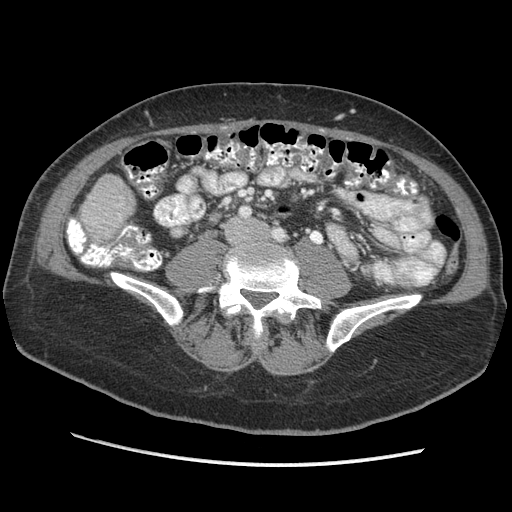
Contrast-enhanced abdominal CT (liver protocol), one axial slice. Position 80 of 170 along the scan axis. Soft-tissue window (W 400 / L 40 HU). 2.5 mm slice thickness. 512 × 512 image matrix, field of view 360 × 360 mm. From the clinical record (not read from this slice): diagnosis: hepatocellular carcinoma (patient treated with transarterial chemoembolisation; whether this scan precedes or follows treatment is not stated here); TNM stage (as recorded): Stage-II; Child-Pugh class: A; tumour differentiation: no biopsy; tumour nodularity: multinodular.
Outlined on this slice (semi-automatic segmentation, software-assisted and operator-edited):
- liver parenchyma outside the tumour (the mass and vessels are separate outlines, so this box may not span the whole liver): bounding box [x1, y1, x2, y2] px = [90, 174, 134, 224]